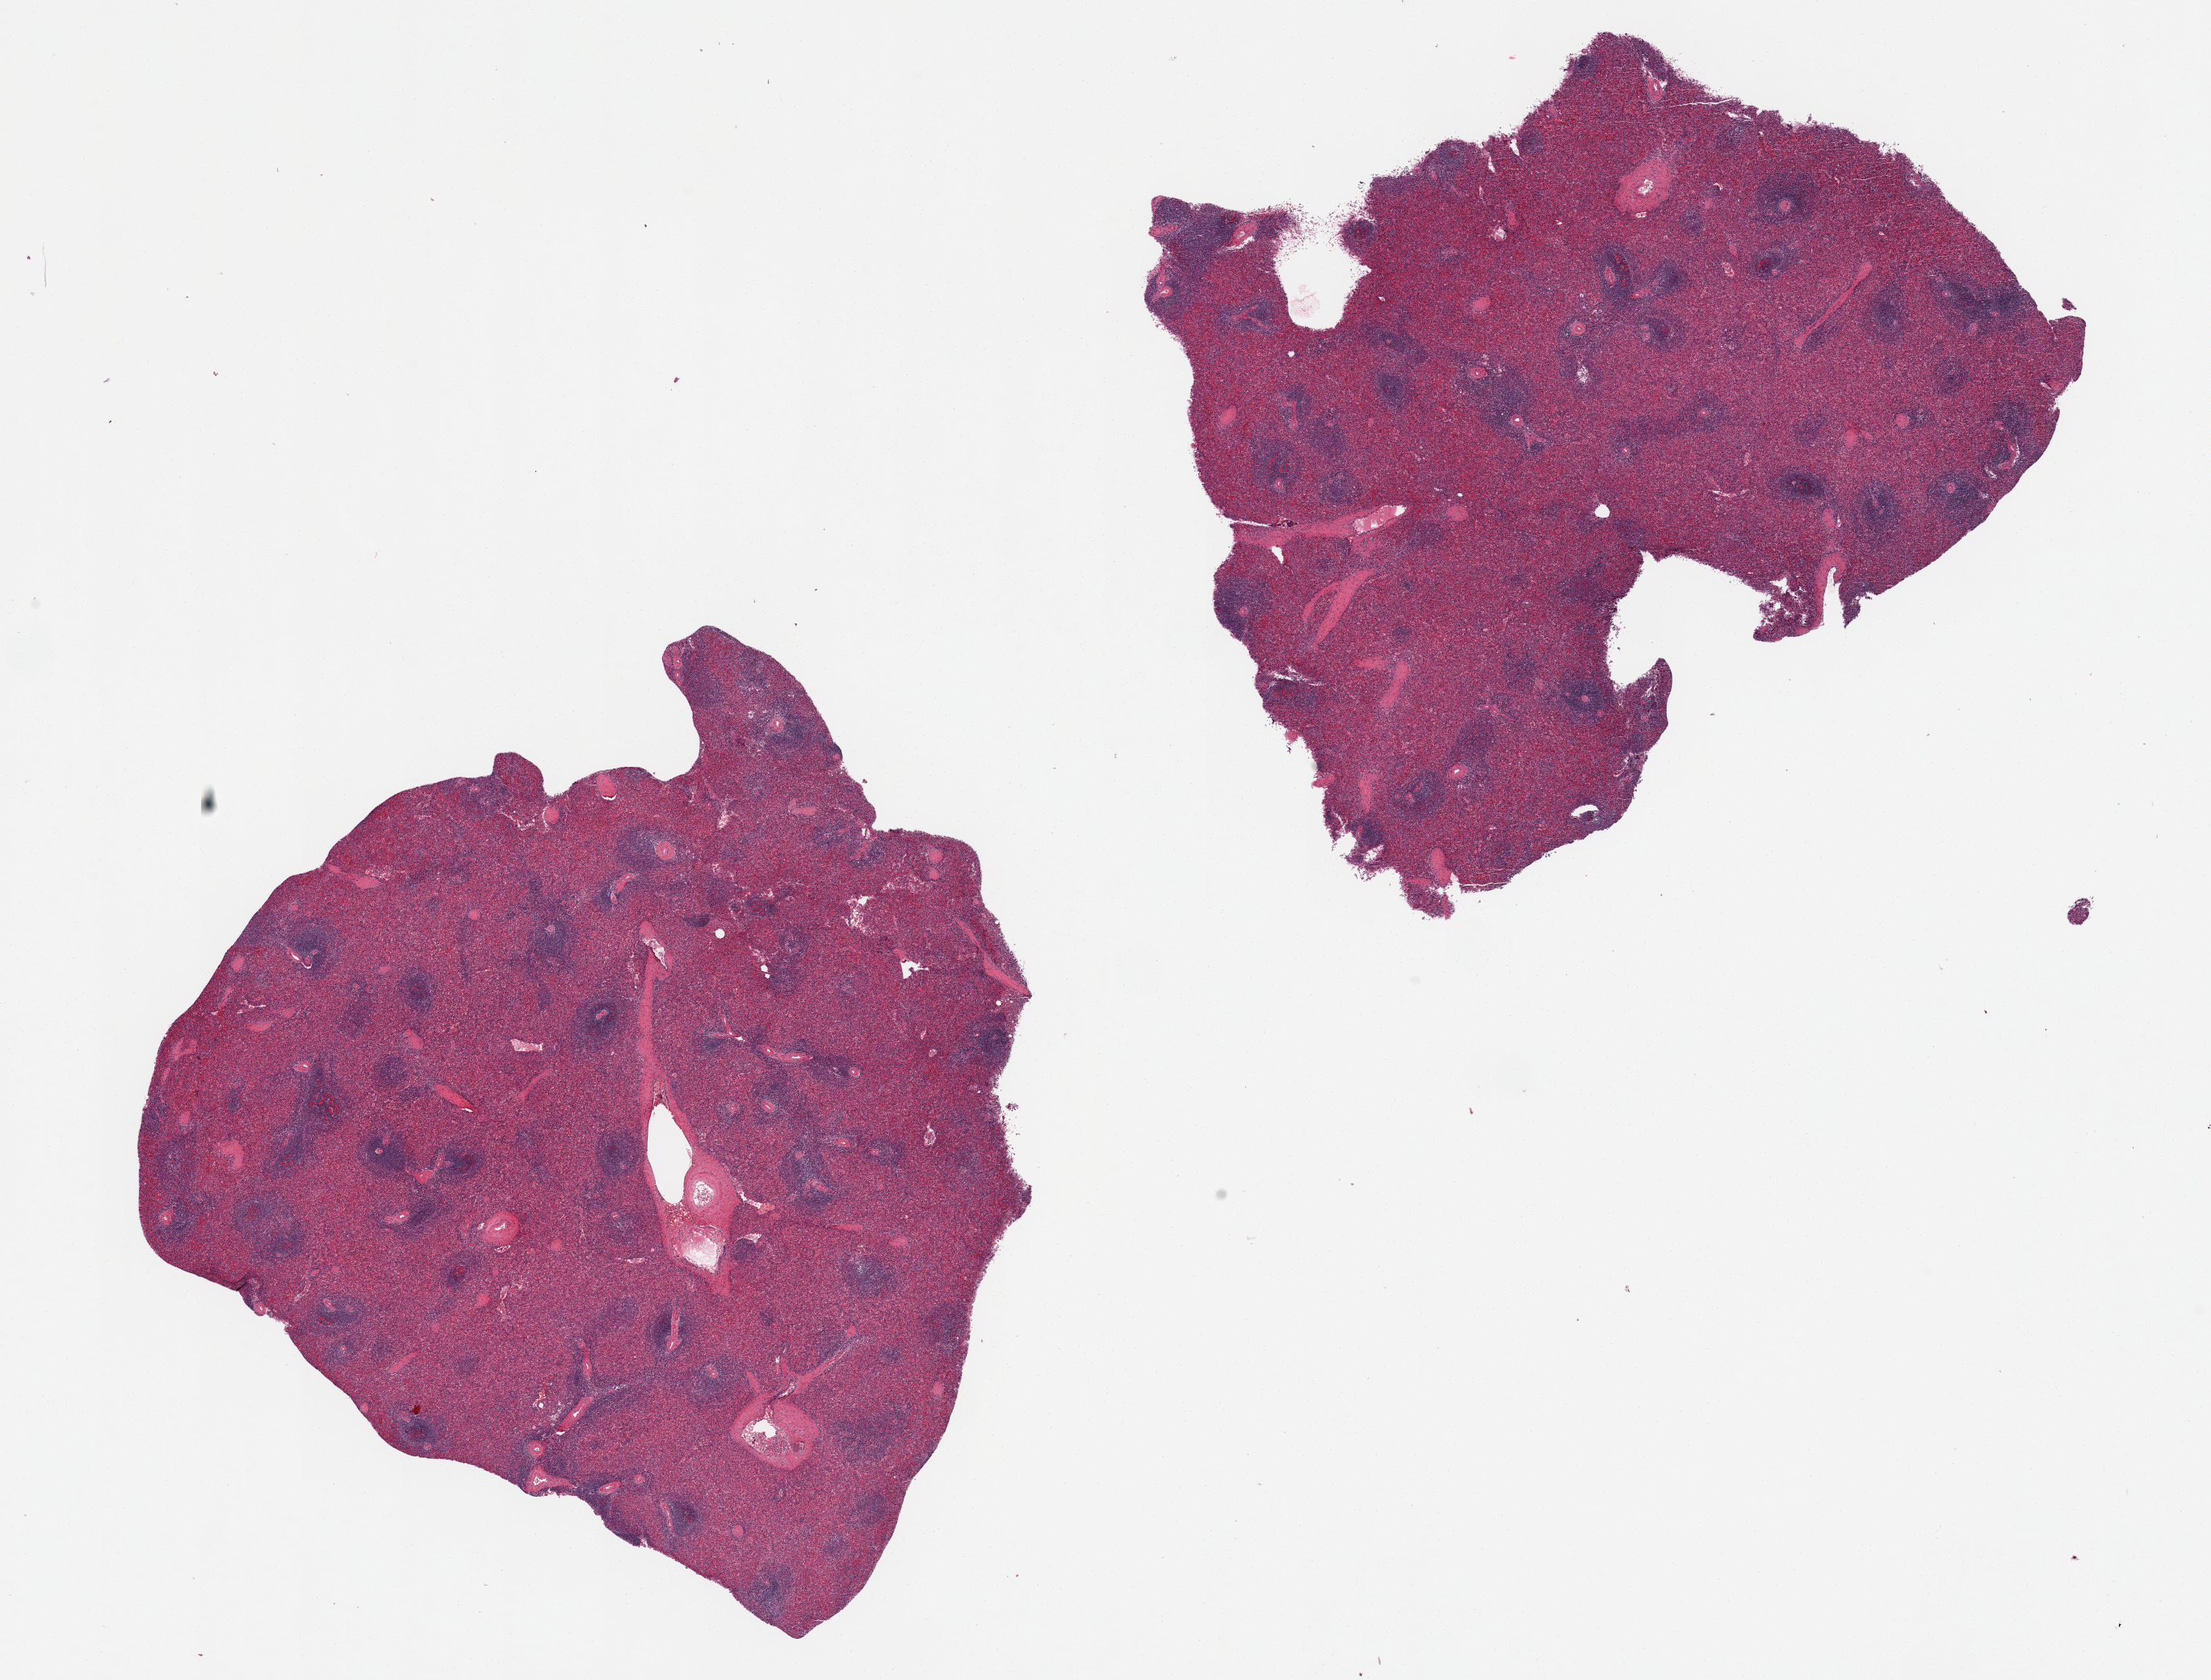
Whole-slide image, haematoxylin and eosin stain — whole scanned area (about 21.7 x 16.5 mm, from a 20x scan) shown as a low-resolution overview; PAXgene-fixed paraffin-embedded (PFPE) section; target tissue: spleen; donor tissue sample.
Review note (as recorded): 2 pieces.